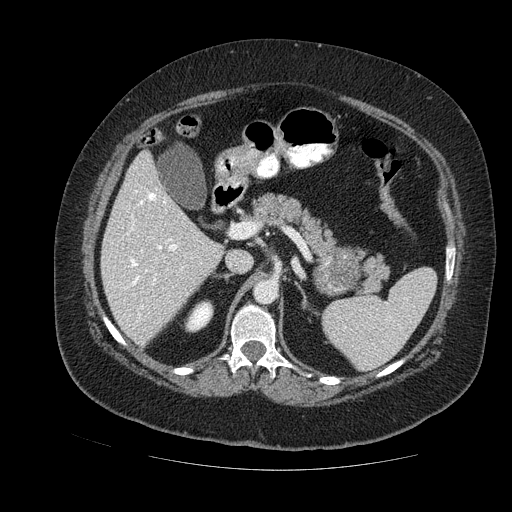
Contrast-enhanced abdominal CT, one axial slice; slice 73 of 121 in the series (ordered by position); soft-tissue window (W 400 / L 40 HU); 512 × 512 image matrix, field of view 420 × 420 mm. Female patient. Case-level facts recorded for this patient, not image findings: diagnosis: adrenocortical carcinoma; tumour side: left adrenal.
Structures marked on this image (semi-automatic segmentation, software-assisted and operator-edited):
- mass: bounding box (x1, y1, x2, y2) in pixels: (317, 247, 360, 294)